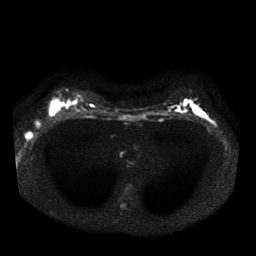
Breast MRI, one axial slice; slice 26 of 41 in the series (ordered by position); diffusion-weighted series; image 2 of 4 stored at this slice position (different b-values; order by instance number); 1.5 T; 5 mm slice thickness; 256 × 256 image matrix, field of view 330 × 330 mm. Female patient.
Annotated regions visible in this slice (expert manual segmentation):
- tumour on diffusion-weighted imaging: bounding box <23,122,38,139> (left, top, right, bottom; pixels)